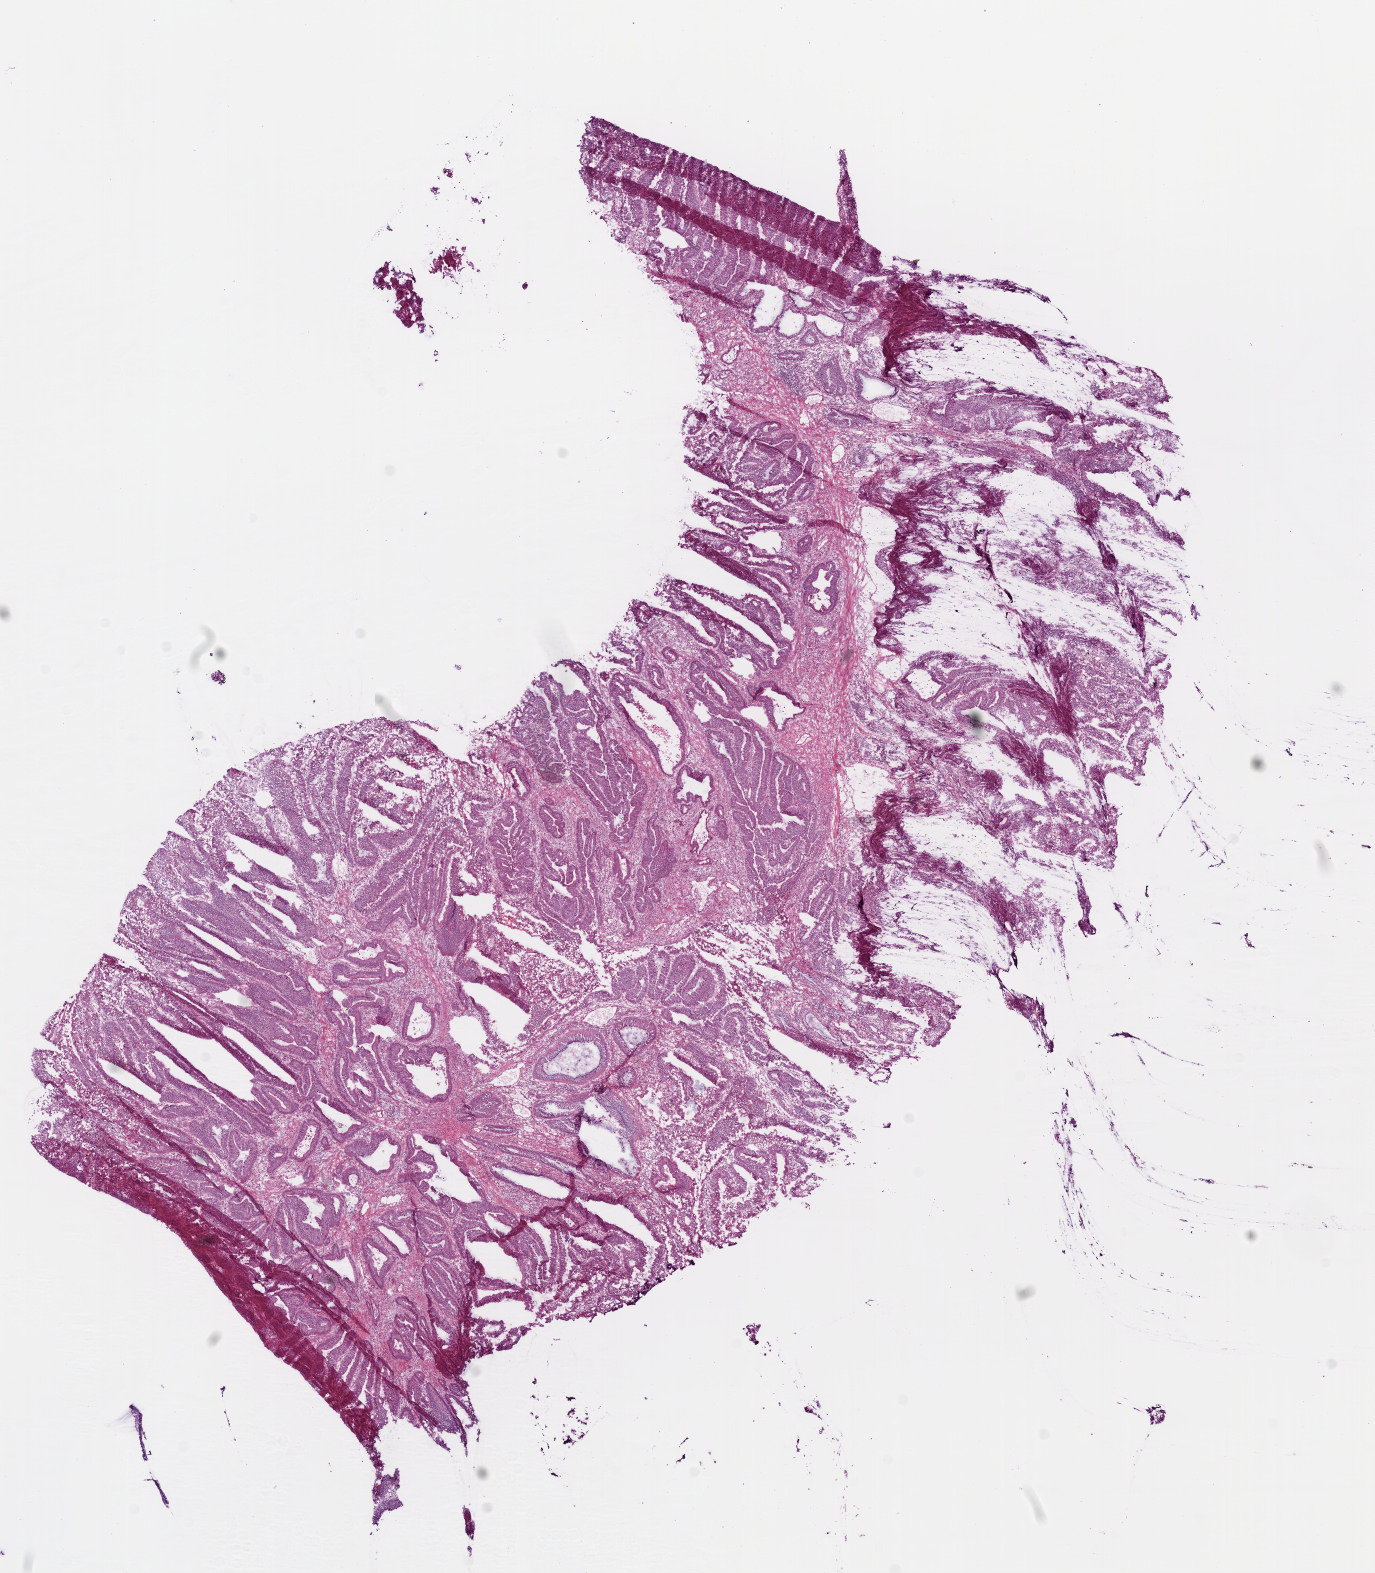
Digitized H&E-stained tissue section (whole slide) — low-resolution overview of the scanned area, about 11.0 x 12.6 mm (acquisition: 20x scan); frozen section from the bottom of the tissue portion; primary tumour sample from the colon. Female, age 78 years at initial diagnosis. Slide review estimates, as recorded: tumour cells 80%, tumour nuclei 85%.
Histologic diagnosis: Adenocarcinoma, NOS.